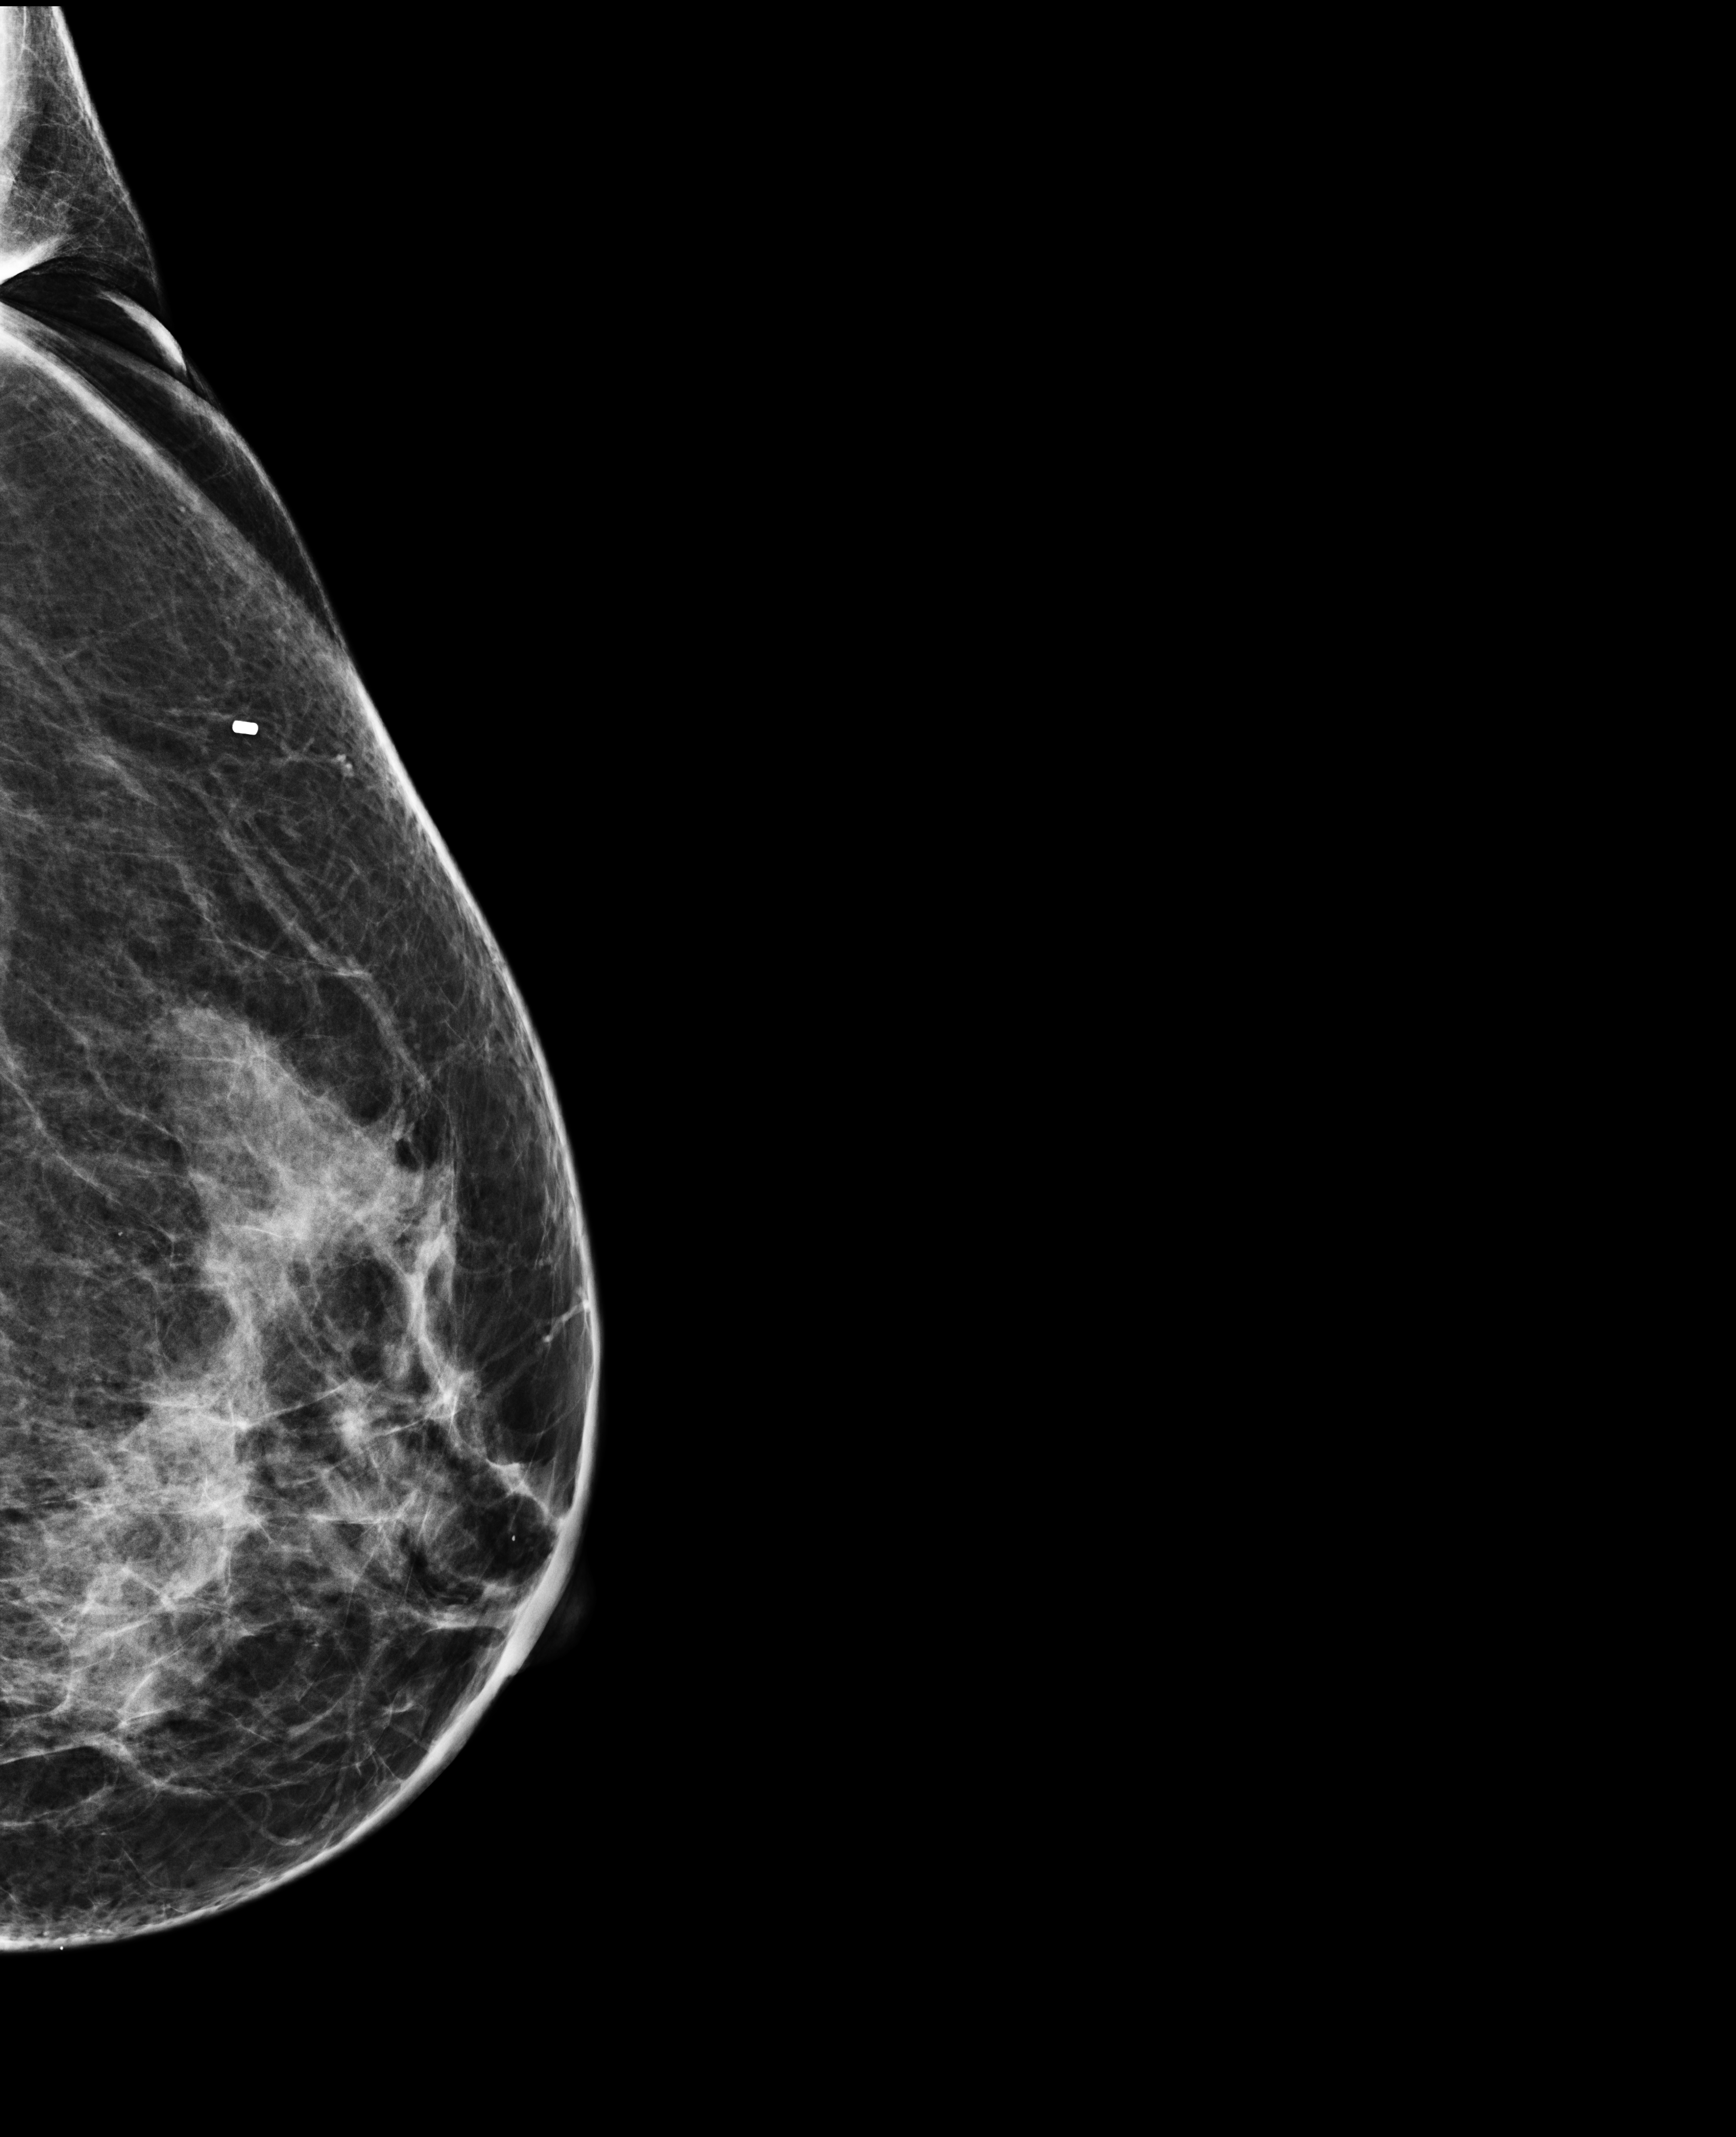
Annual screening mammography examination. Patient aged 47 years (female).
Image type: full-field digital mammogram. Breast: left. Projection: exaggerated CC view (lateral).